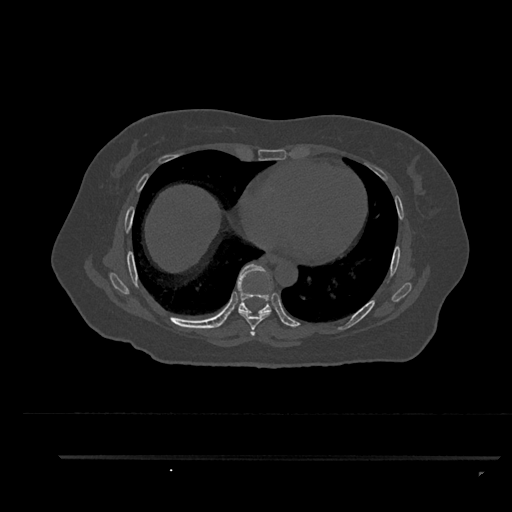
CT including the spine, one axial slice; slice 487 of 797 in the series (ordered by position); reconstruction kernel Br40s/3; bone window (W 1800 / L 400 HU); 0.5 mm slice thickness; 512 × 512 image matrix. Female patient, age 44 years. From the clinical record (not read from this slice): primary cancer: renal; vertebrae with lytic lesions (as recorded): L1.
Annotated regions visible in this slice (semi-automatic segmentation, software-assisted and operator-edited):
- T6 vertebra: bounding box <252,333,254,335> (left, top, right, bottom; pixels)
- T7 vertebra: <238,310,271,336>
- T8 vertebra: <237,264,281,320>